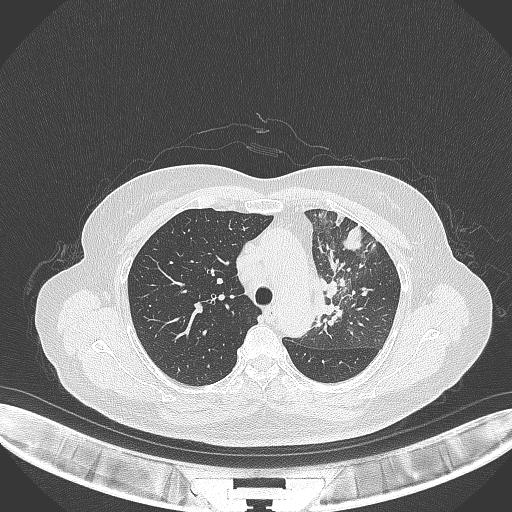
Chest CT, one axial slice. Reconstruction kernel B70f. 120 kVp. Lung window (W 1500 / L -600 HU). 1 mm slice thickness. 512 × 512 image matrix, field of view 400 × 400 mm. Patient: female, 64 years. Case-level facts recorded for this patient, not image findings: clinical TNM (as recorded): T2a N2 M0.
Annotated regions visible in this slice (rectangle marked by the reading radiologist):
- lung tumour (recorded histology: adenocarcinoma): bounding box <312,268,349,328> (left, top, right, bottom; pixels)
- lung tumour (recorded histology: adenocarcinoma): <340,221,370,253>